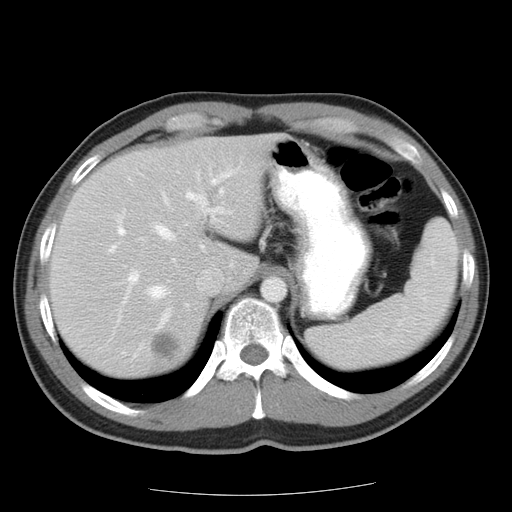
Contrast-enhanced abdominal CT, one axial slice. Slice 15 of 22 in the series (ordered by position). Intravenous contrast given. Soft-tissue window (W 400 / L 40 HU). 512 × 512 image matrix, field of view 359 × 359 mm. Male patient, age 41 years. From the clinical record (not read from this slice): diagnosis: colorectal cancer liver metastases, imaged before liver resection; multiple liver metastases: no; largest metastasis: 2.7 cm; disease in both lobes: no.
Structures marked on this image (manually delineated by an expert):
- hepatic veins: bounding box [x1, y1, x2, y2] px = [149, 190, 224, 327]
- liver: [51, 137, 269, 375]
- planned liver remnant (the part of the liver to remain after resection): [51, 137, 269, 340]
- portal vein (with intrahepatic branches): [117, 172, 232, 322]
- liver metastasis: [147, 328, 184, 364]